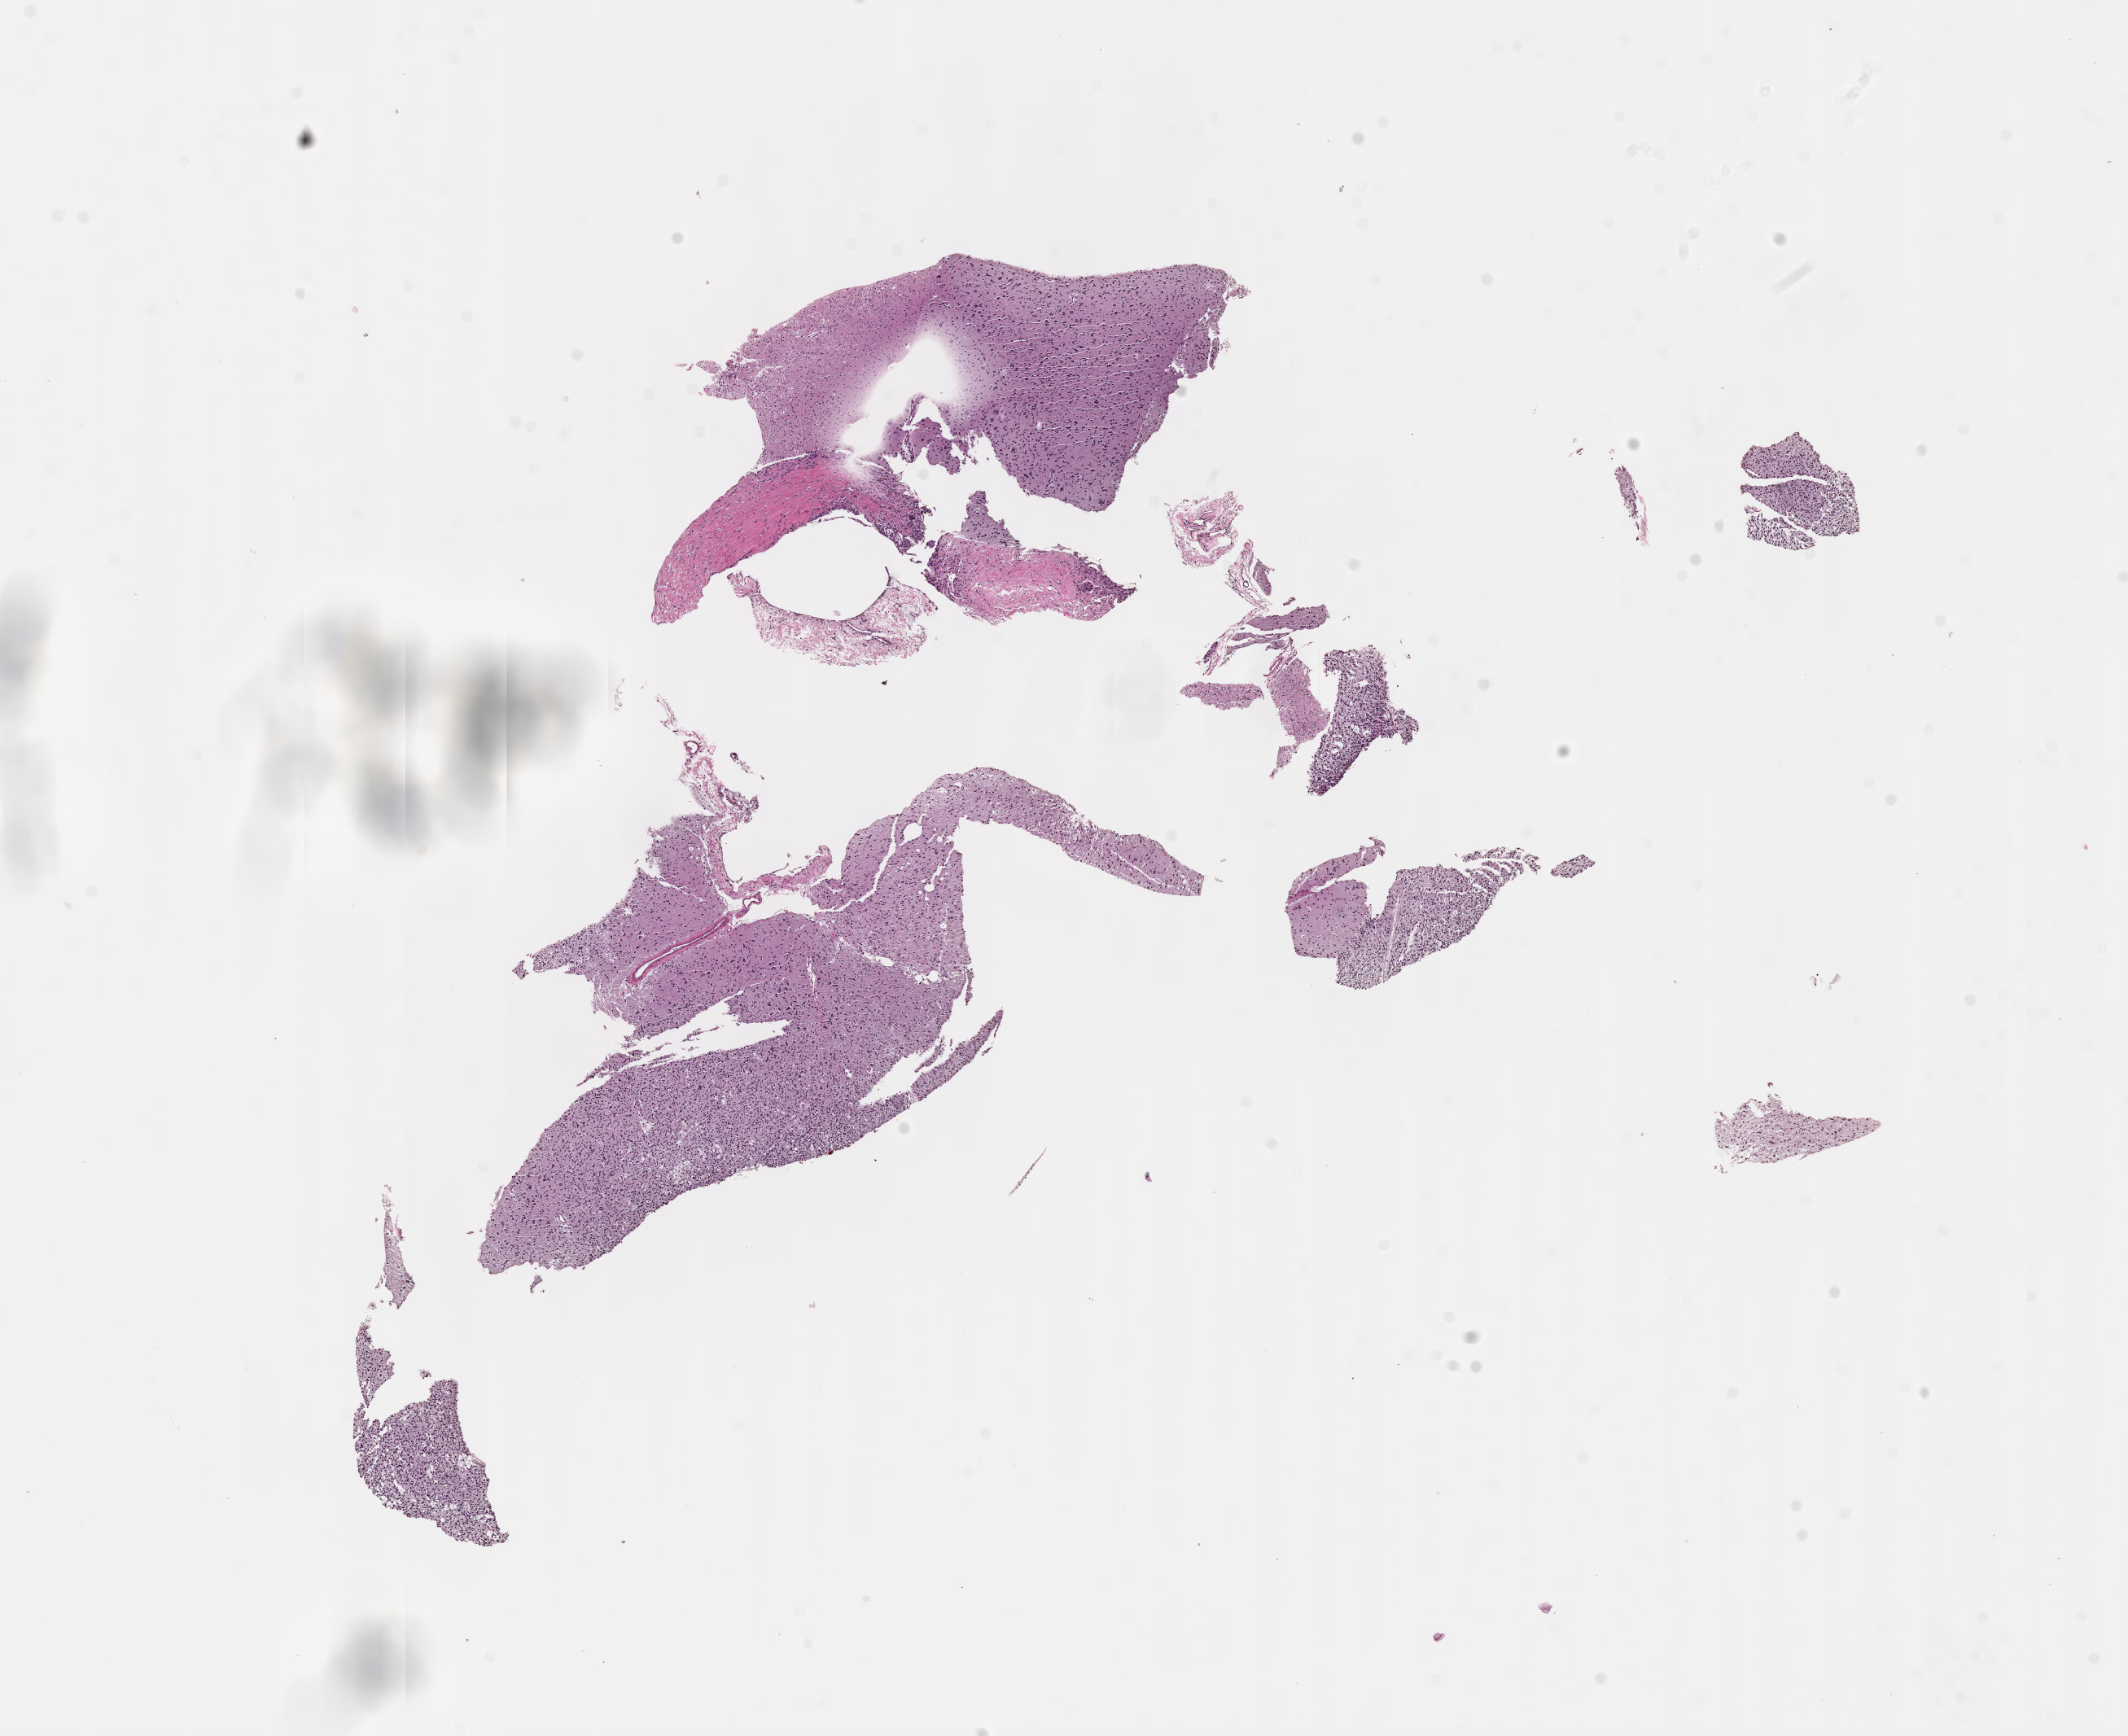
Digitized Hematoxylin and eosin (H&E) stained tissue section (whole slide), whole scanned area (about 10.6 x 8.6 mm) shown as a low-resolution overview; formalin-fixed paraffin-embedded (FFPE) diagnostic section; primary tumour sample from the brain. Patient: female, age at initial diagnosis 35 years. Histologic grade: G2 (moderately differentiated).
Diagnosis: Mixed glioma (cerebrum).